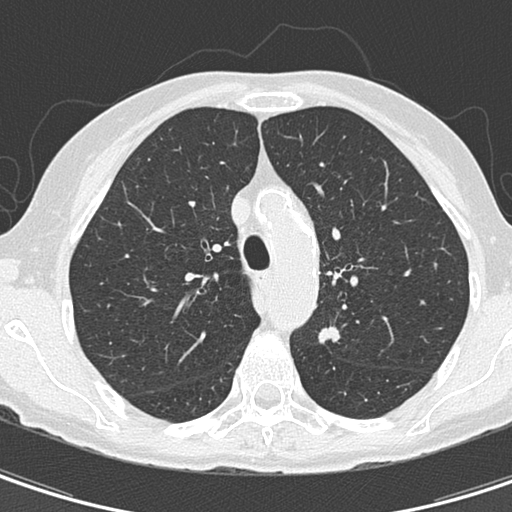
Low-dose screening chest CT, axial slice; baseline annual screen; lung window (W 1500 / L -600 HU); 2 mm slice thickness; slice 48 of 157 in the series; 512 × 512 image matrix, field of view 260 × 260 mm. Female participant, aged 67 years at enrolment. Current smoker at enrolment.
Expert reader's lesion annotation, bounding box <298,316,357,363> (left, top, right, bottom; pixels). Screening reader's record for this exam (one nodule recorded; not confirmed to be the boxed lesion): non-calcified nodule or mass ≥4 mm, left upper lobe, 11 × 8 mm, spiculated (stellate) margins, soft tissue attenuation. Later outcome: lung cancer diagnosed 73 days after this screen — adenocarcinoma, NOS, left upper lobe, poorly differentiated (G3), stage IA (AJCC 6th edition), 13 mm at pathology.